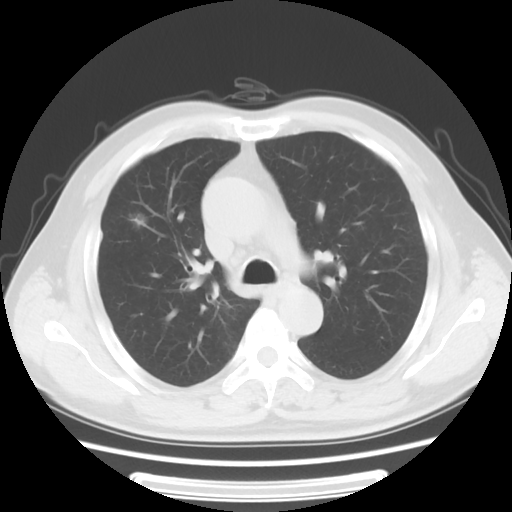
Chest CT, one axial slice. Position 40 of 63 along the scan axis. 120 kVp. Lung window (W 1500 / L -600 HU). 5 mm slice thickness. 512 × 512 image matrix, field of view 360 × 360 mm. Patient: male, 63 years. From the clinical record (not read from this slice): clinical TNM (as recorded): T1c N0 M0.
Structures marked on this image (rectangle marked by the reading radiologist):
- lung tumour (recorded histology: adenocarcinoma): box from (x=125, y=209) to (x=157, y=237) px